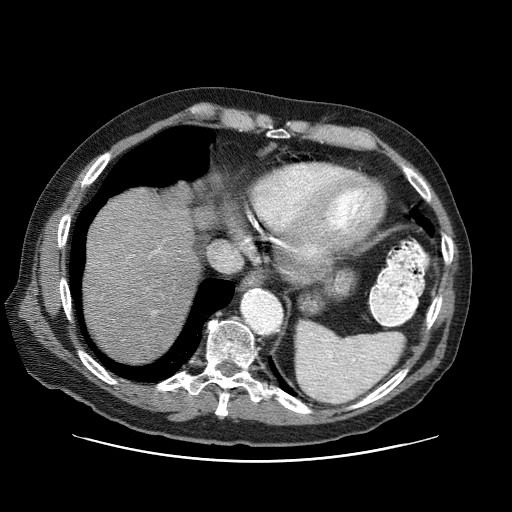
Contrast-enhanced abdominal CT (liver protocol), one axial slice; position 66 of 87 along the scan axis; one of 3 acquisitions stored at this slice position; soft-tissue window (W 400 / L 40 HU); 2.5 mm slice thickness; 512 × 512 image matrix, field of view 400 × 400 mm. Case-level facts recorded for this patient, not image findings: diagnosis: hepatocellular carcinoma (patient treated with transarterial chemoembolisation; whether this scan precedes or follows treatment is not stated here); TNM stage (as recorded): Stage-IIIA; Child-Pugh class: A; tumour differentiation: well differentiated; tumour nodularity: multinodular.
Outlined on this slice (semi-automatically segmented with operator editing):
- liver parenchyma outside the tumour (the mass and vessels are separate outlines, so this box may not span the whole liver): bounding box [x1, y1, x2, y2] px = [84, 188, 218, 362]
- liver vessels: [132, 249, 159, 256]